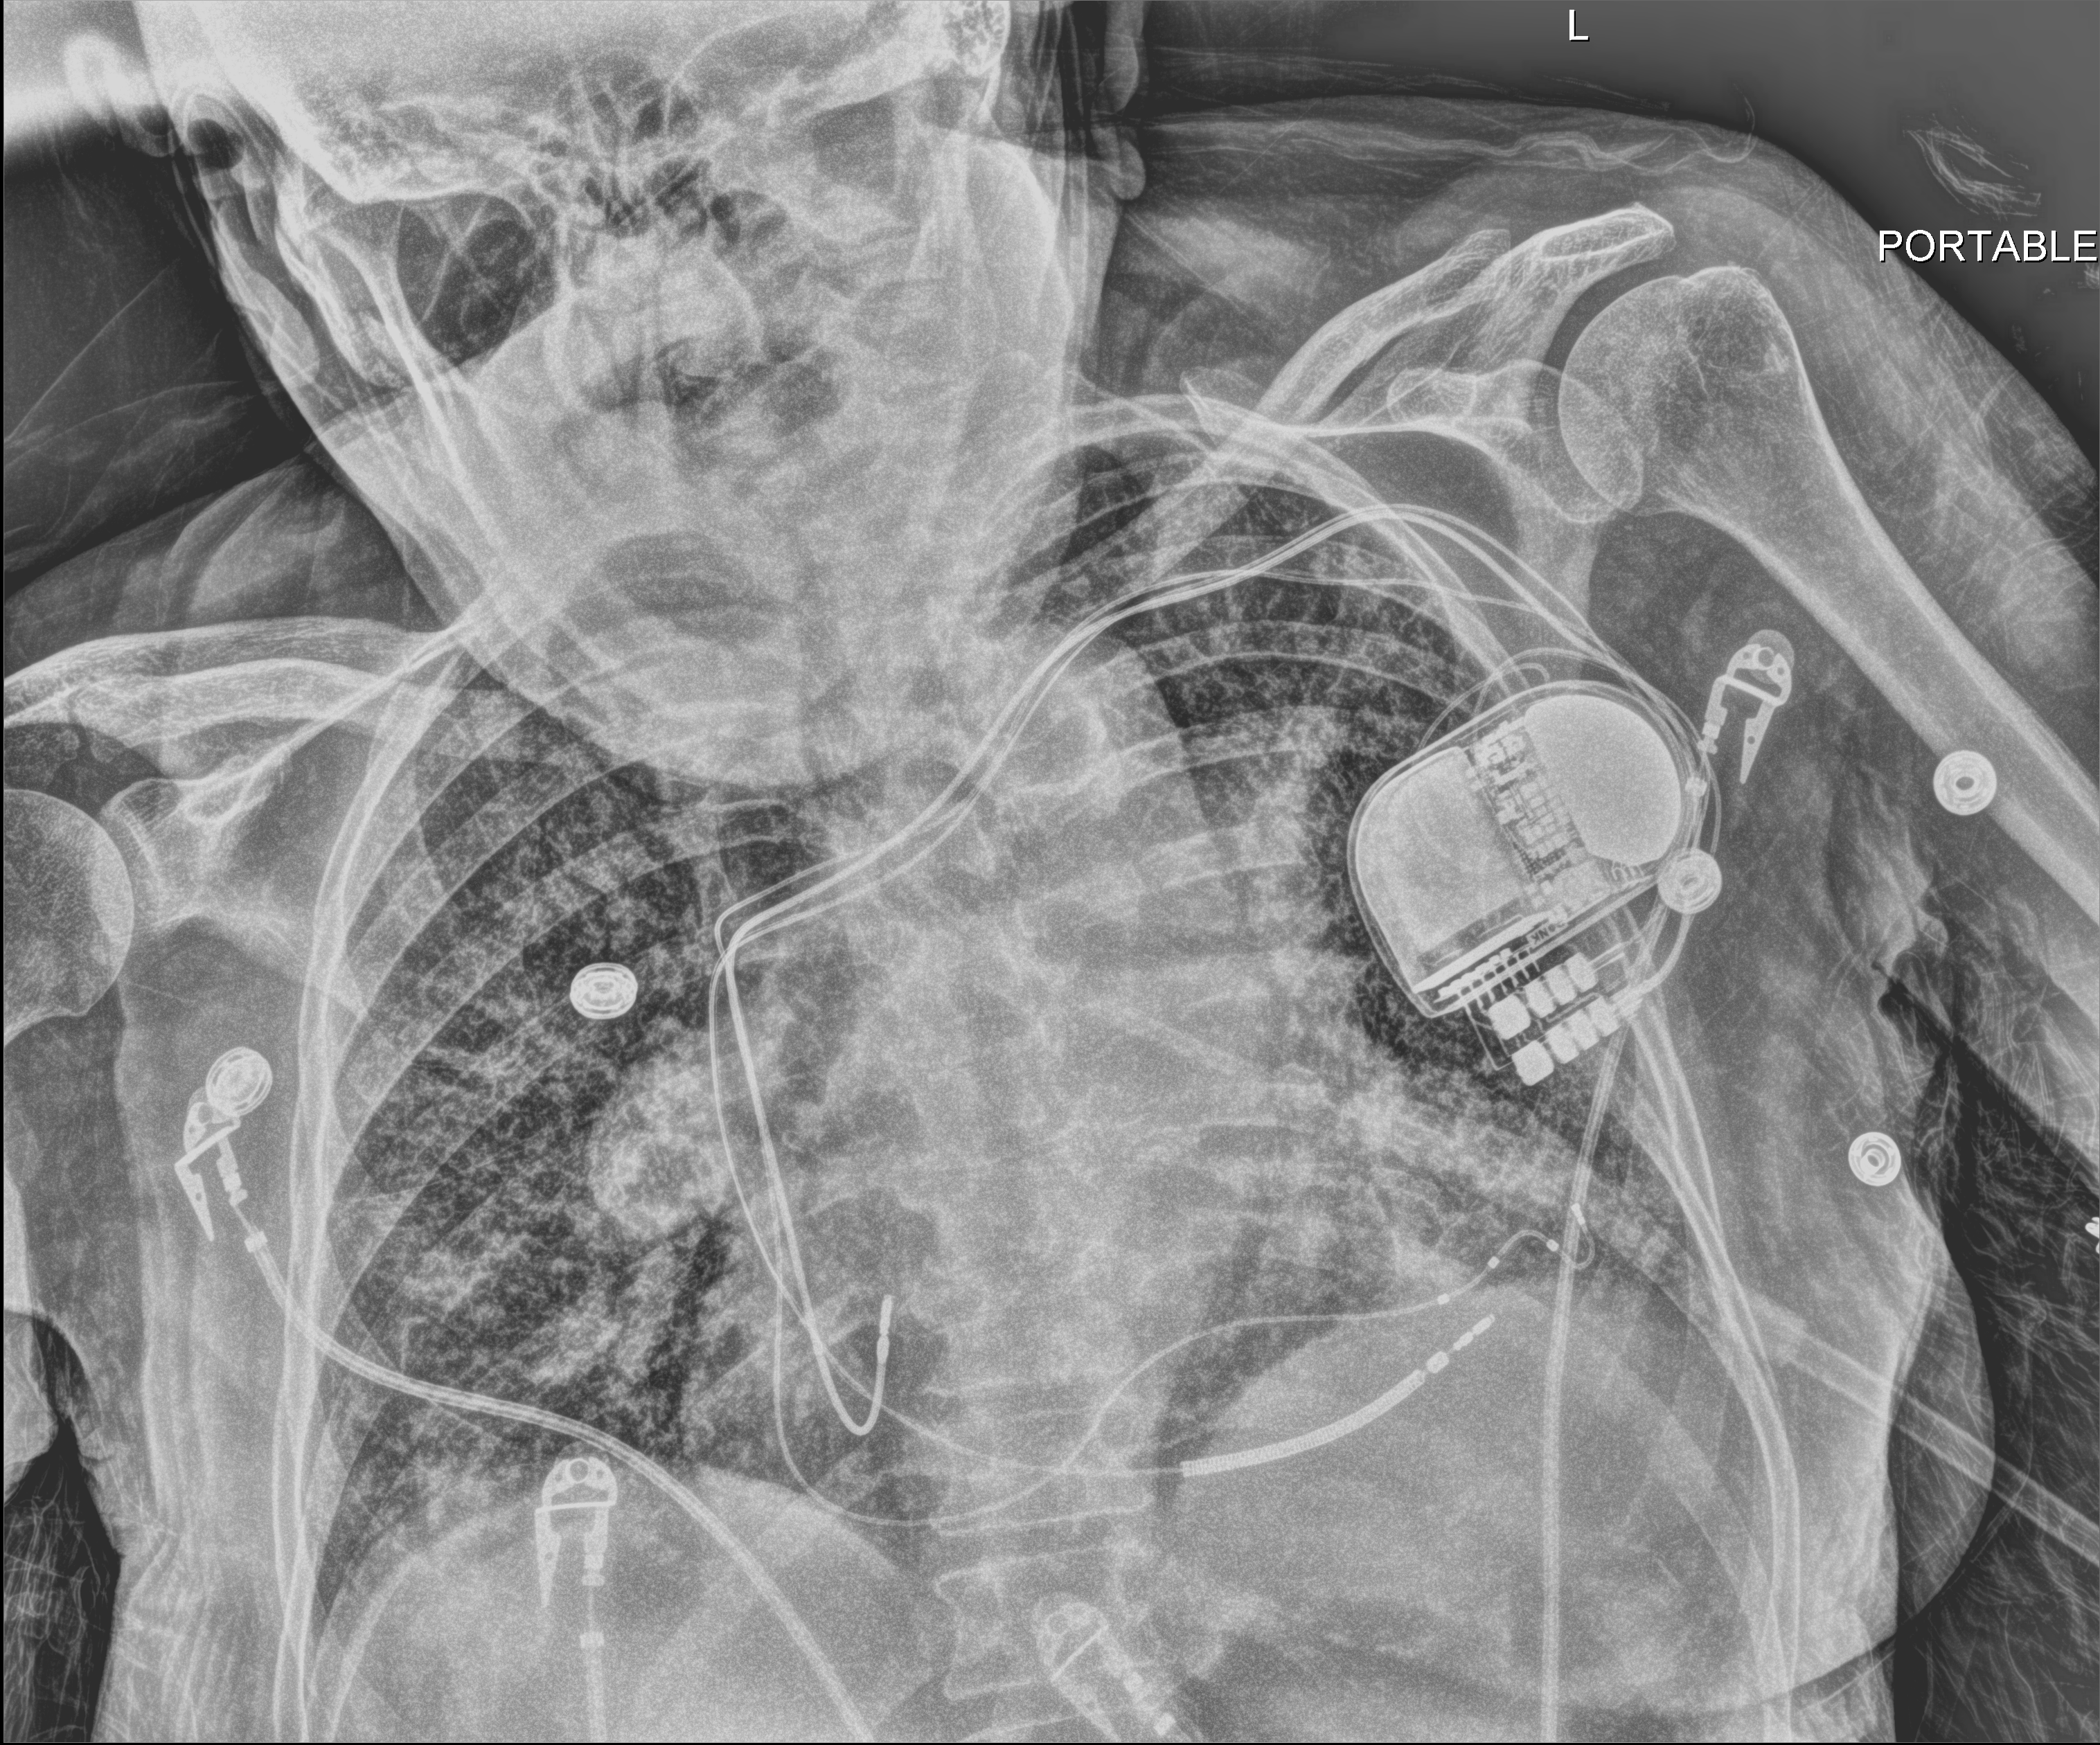
Bedside chest radiograph (digital radiography). Female patient hospitalised with COVID-19, age 60–74 years.
Admission-level facts for this patient (not findings on this image; timing relative to this image not recorded): length of hospital stay: 6 days; mechanically ventilated during this hospital stay: no; admitted to intensive care during this hospital stay: yes.